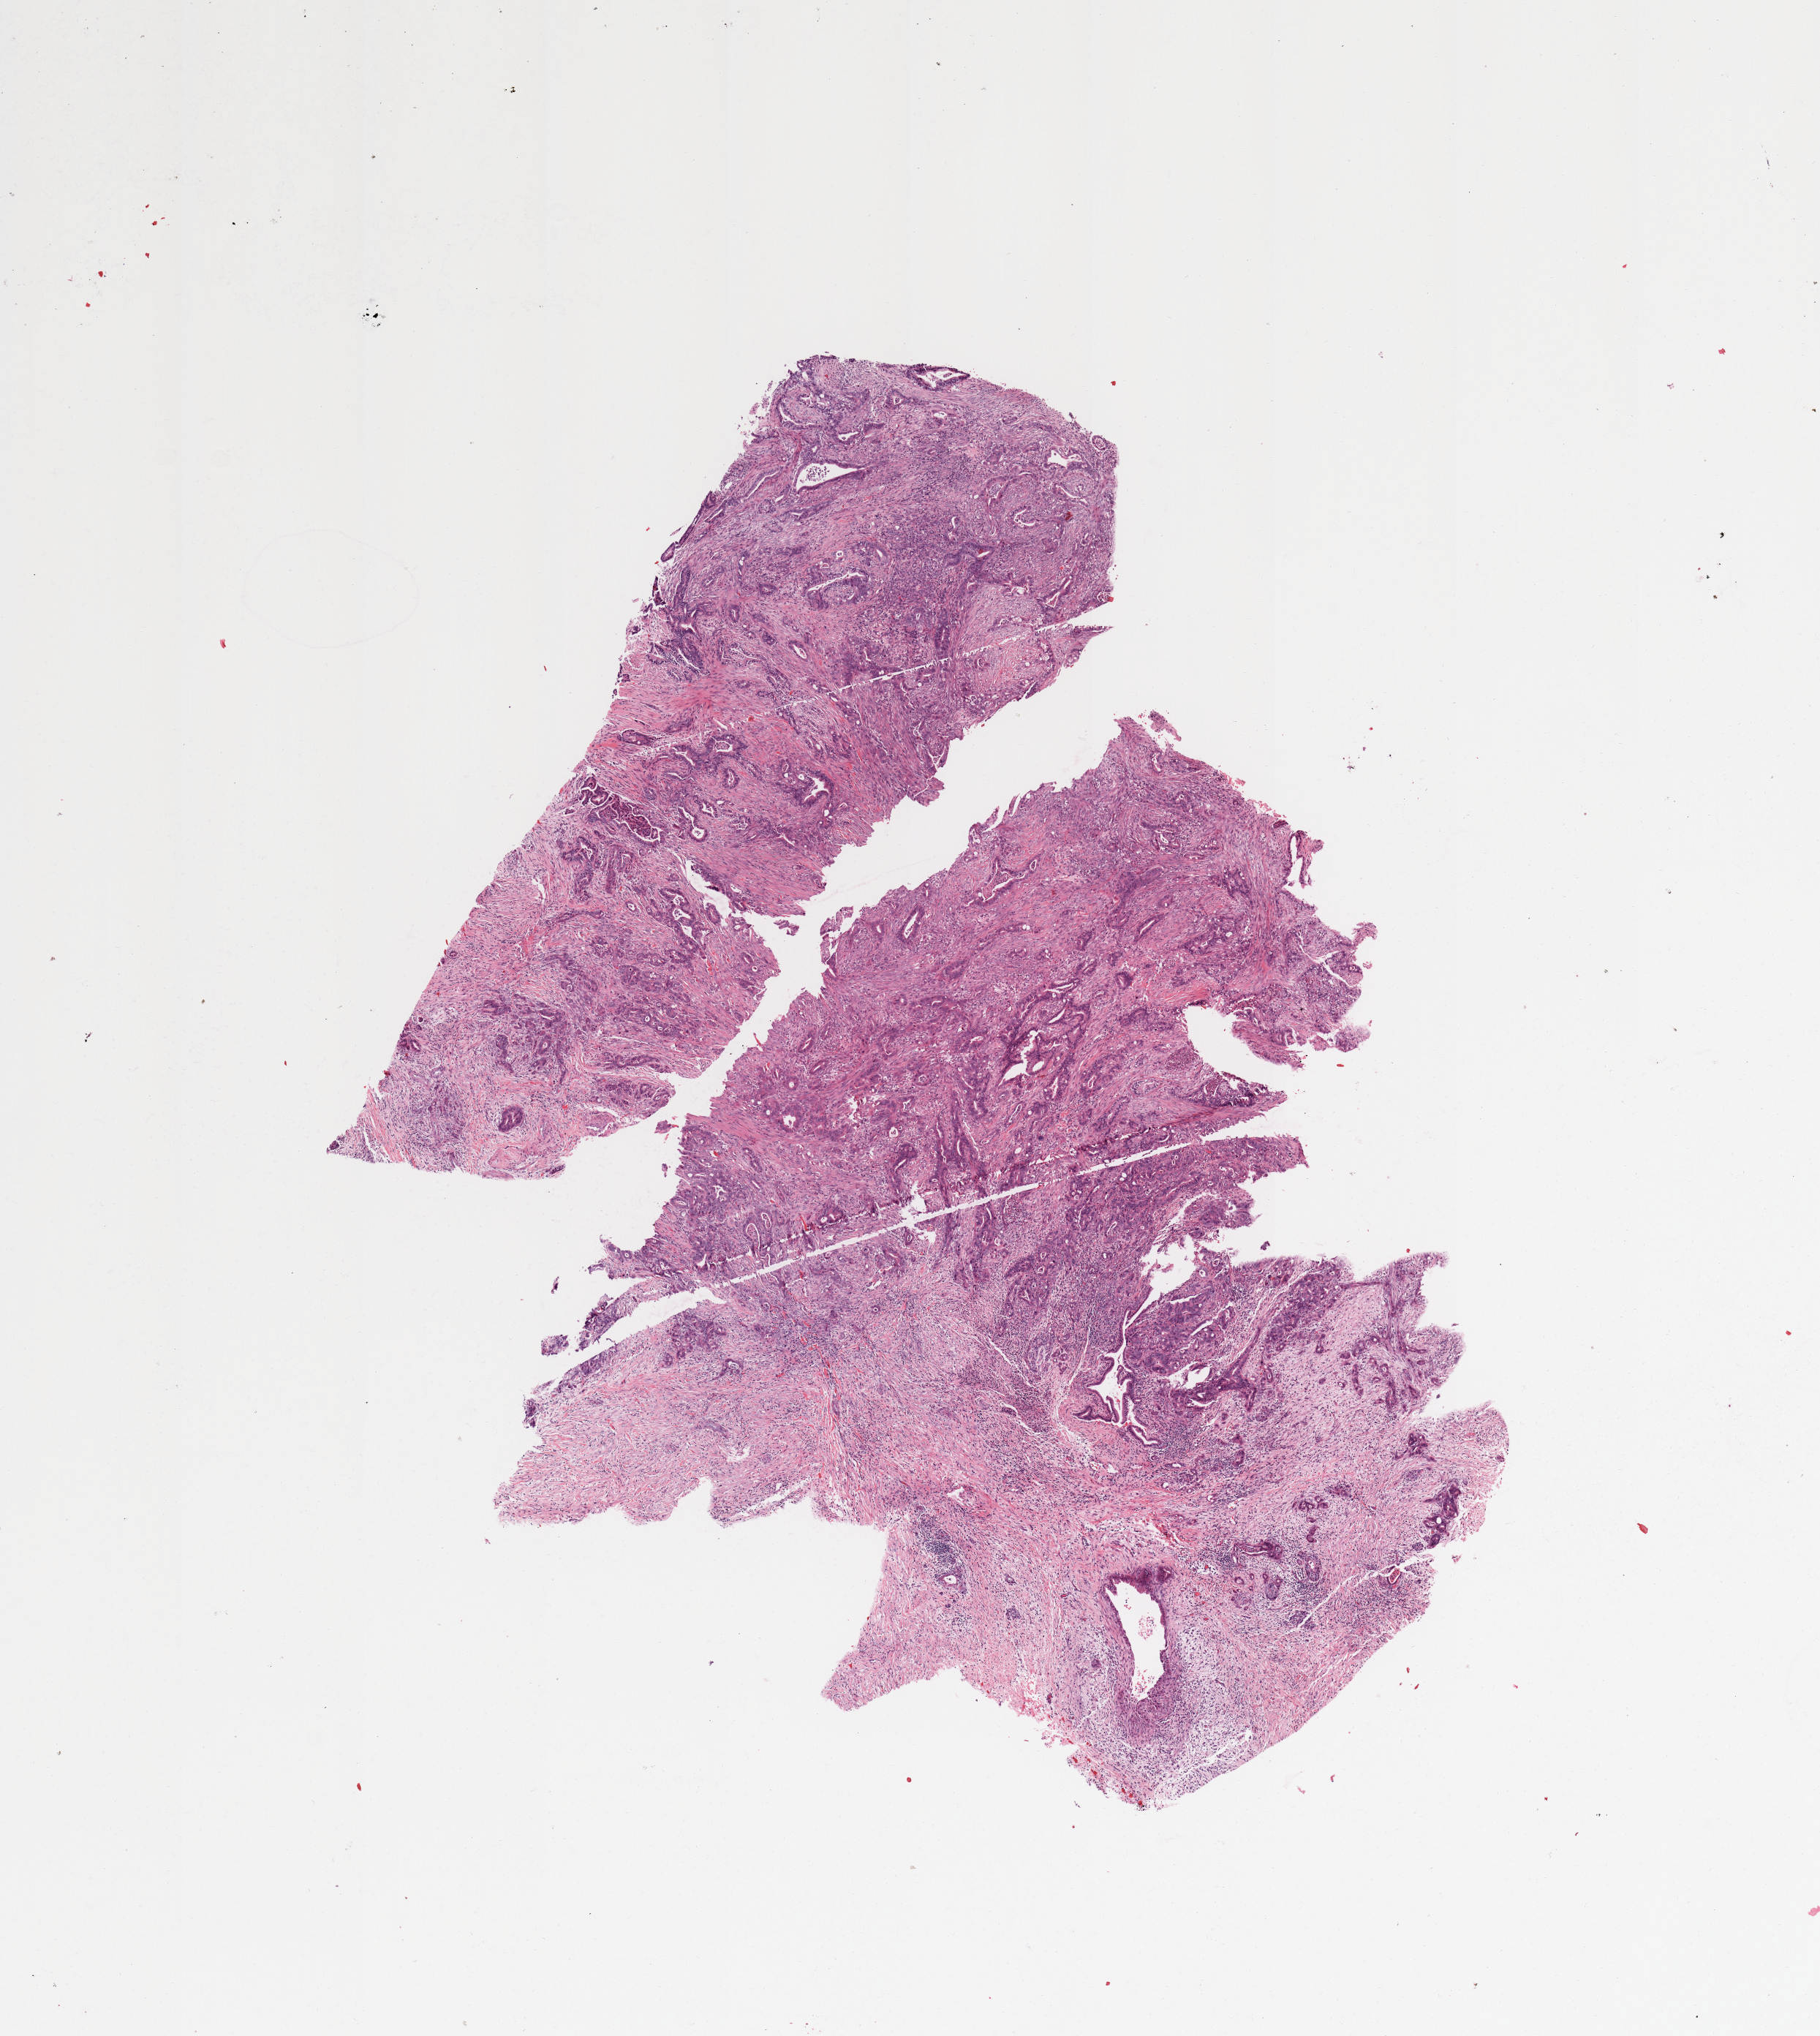
Hematoxylin and eosin (H&E) stained whole-slide image, low-resolution overview of the scanned area, about 9.8 x 11.0 mm (from a 20x scan); tumour tissue sample, sampled site: pancreas. 62-year-old female patient. Histologic grade: G3 (poorly differentiated). Composition of this section per pathologist review: tumour nuclei 60%, necrosis 0%.
- diagnosis: Infiltrating duct carcinoma, NOS
- primary tumour site (as recorded): body
- AJCC pathologic stage: IIB